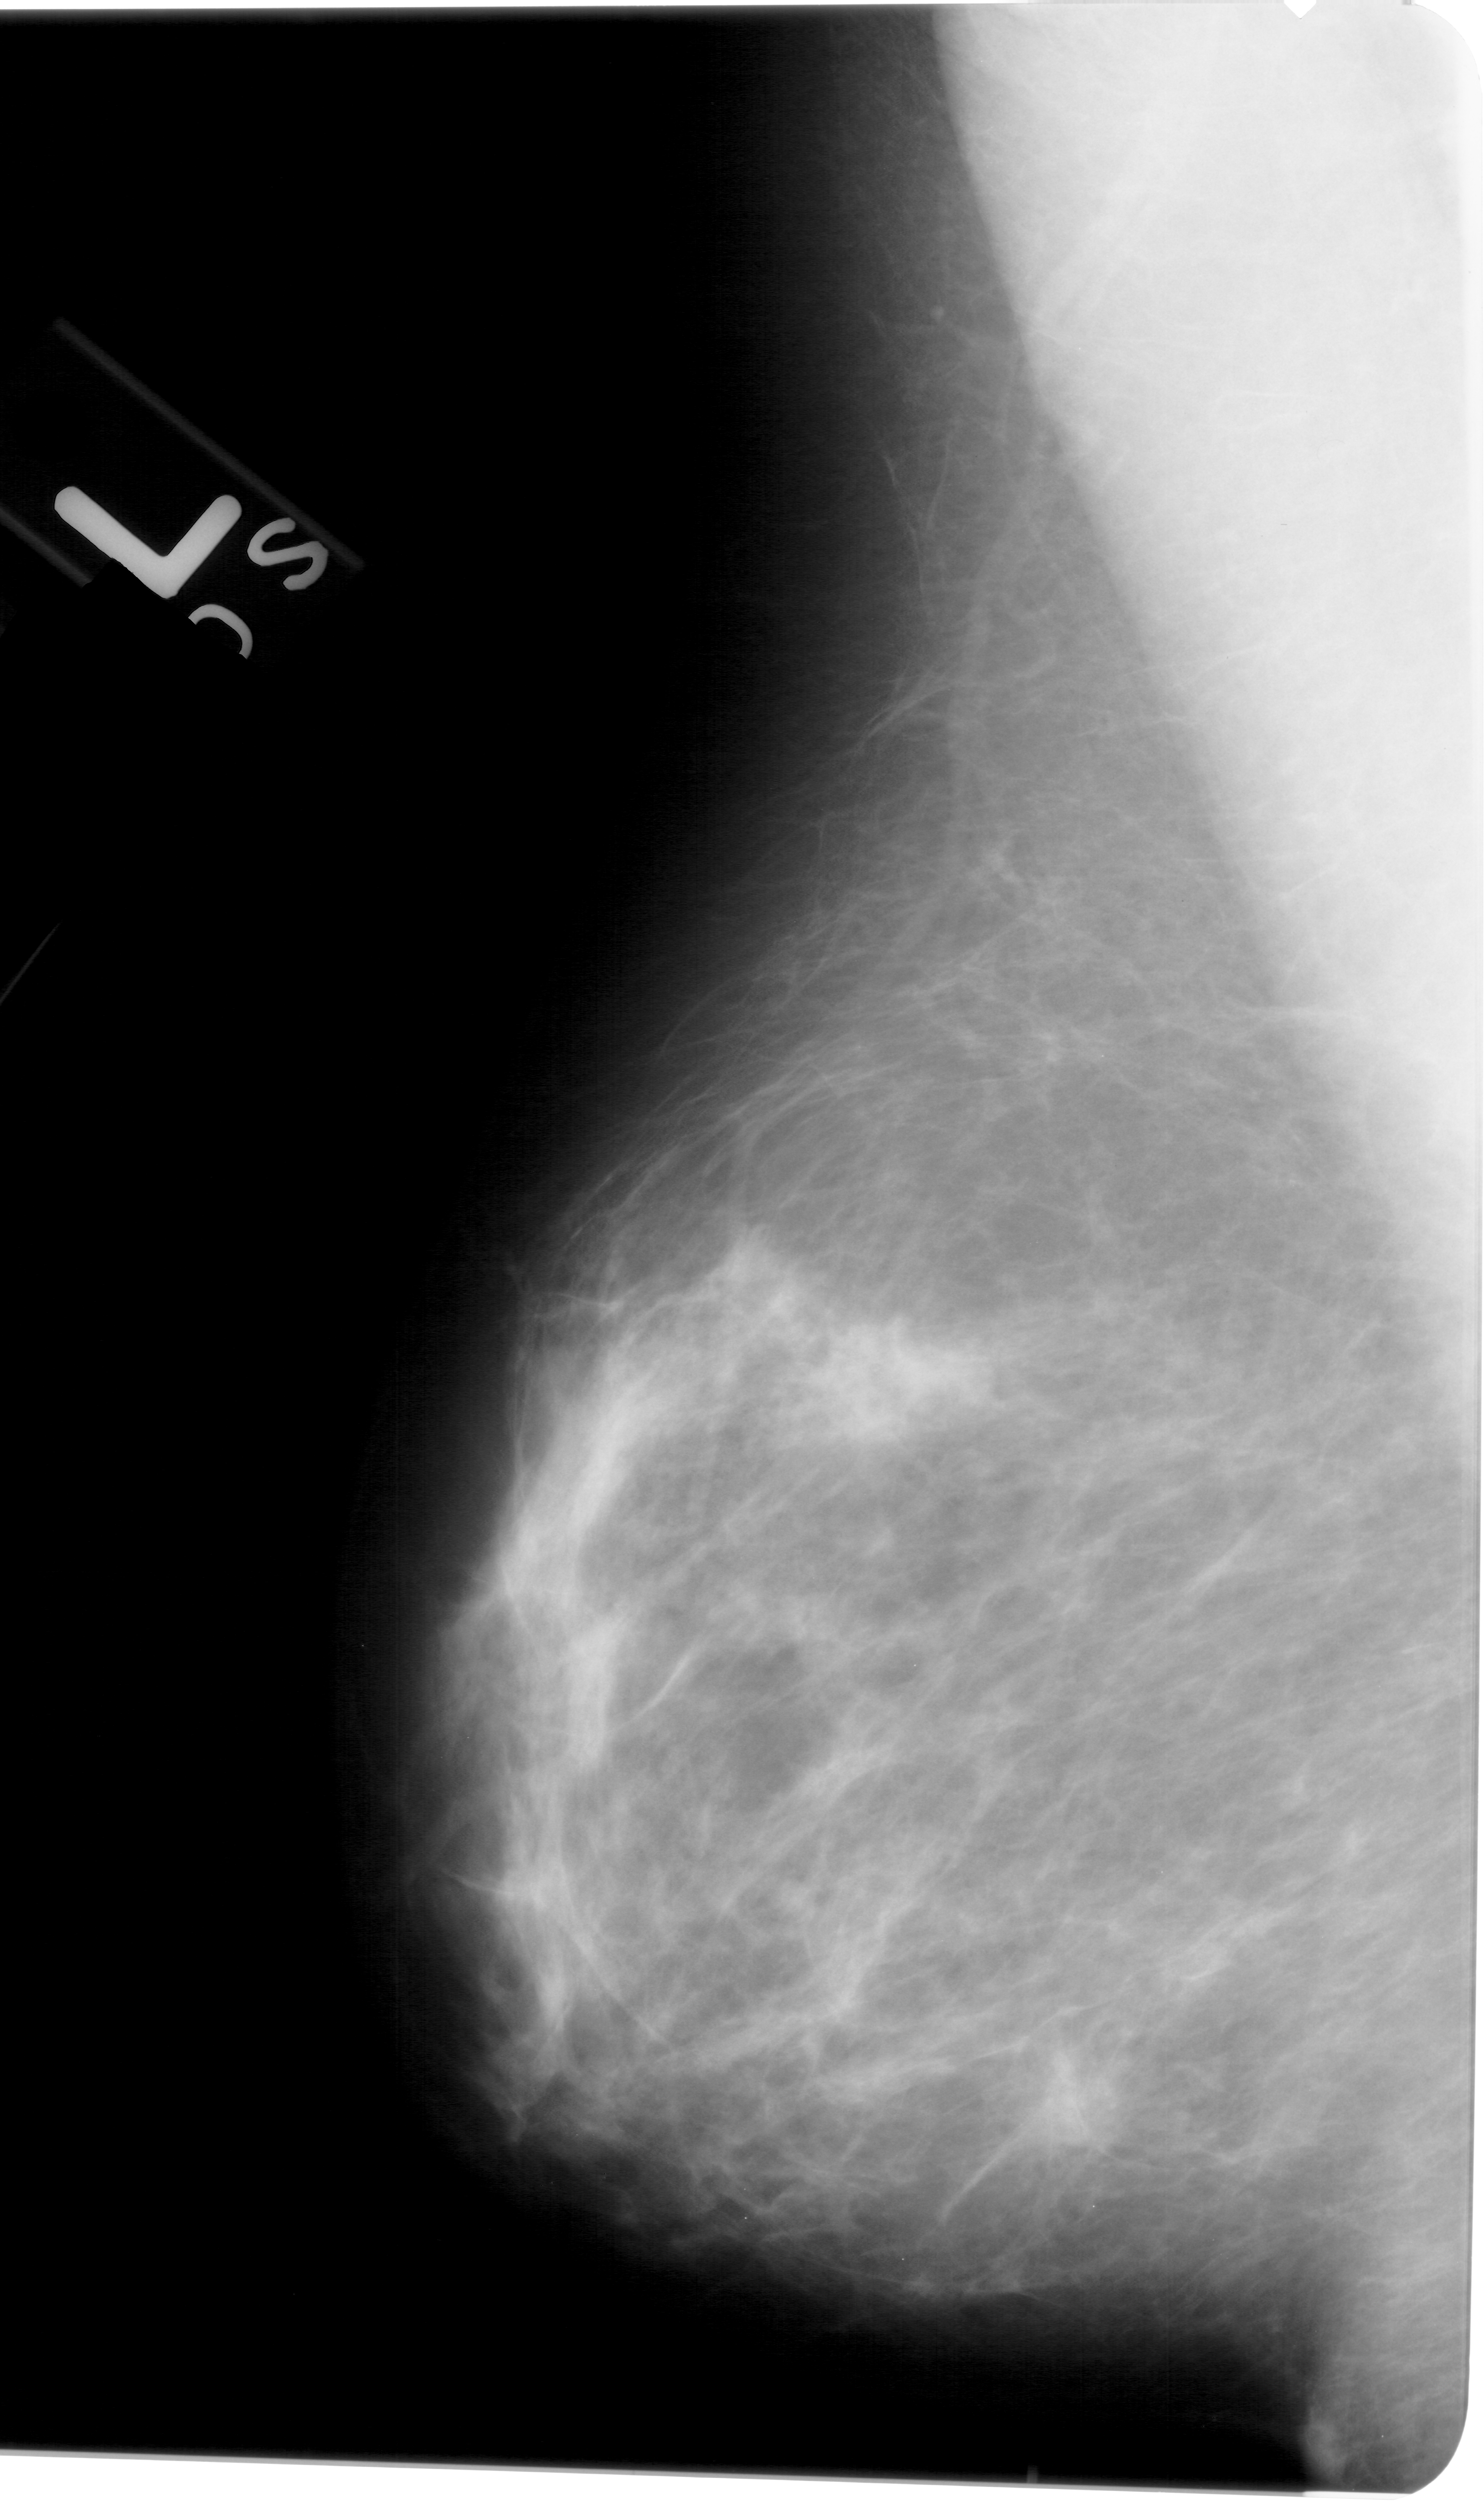
Scanned film-screen mammogram. Left breast. Mediolateral oblique (MLO) view. Breast composition: heterogeneously dense (BI-RADS density category 3 of 4). 1484 × 2503 image matrix.
Expert-marked regions of interest on this image (one box per marked abnormality):
- mass, shape oval, margins obscured / ill defined; BI-RADS assessment category 4; subtlety rating 2 on a 1 (subtle) to 5 (obvious) scale; pathology result (as recorded, not read from the image): benign: bounding box (x1, y1, x2, y2) in pixels: (842, 1308, 991, 1435)